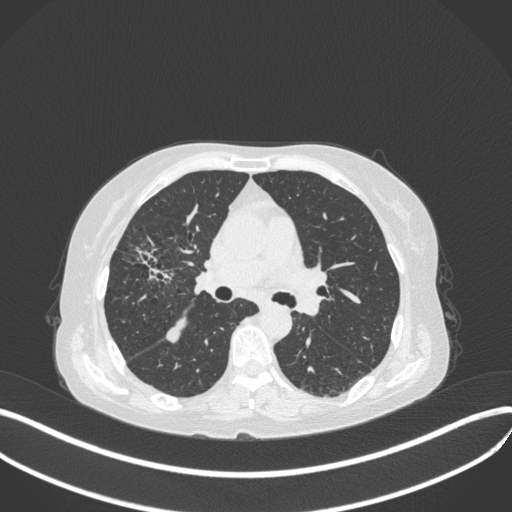
Chest CT, one axial slice. Reconstruction kernel B31f. 120 kVp. Lung window (W 1500 / L -600 HU). 1 mm slice thickness. 512 × 512 image matrix, field of view 400 × 400 mm. Patient: female, 69 years. From the clinical record (not read from this slice): clinical TNM (as recorded): T1b N3 M0.
Annotated regions visible in this slice (bounding box drawn by a radiologist):
- lung tumour (recorded histology: small cell carcinoma): bounding box <127,240,180,293> (left, top, right, bottom; pixels)